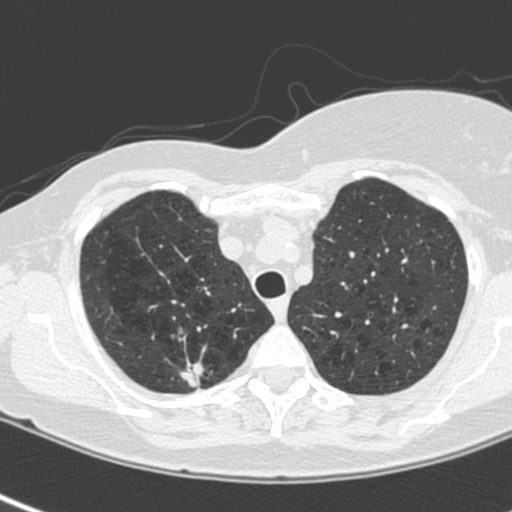
Chest CT (low-dose screening protocol), one axial image. Baseline screening round. Lung window (W 1500 / L -600 HU). 120 kVp. 512 × 512 image matrix. Female participant, aged 64 years at enrolment. Current smoker at enrolment.
Expert reader's lesion annotation, box from (x=167, y=352) to (x=222, y=402) px. The exam's reader record, not a measurement of the box and not confirmed to be the same lesion: non-calcified nodule or mass ≥4 mm, right upper lobe, 13 × 10 mm, spiculated (stellate) margins, soft tissue attenuation. Later outcome: lung cancer diagnosed 21 days after this screen — adenocarcinoma, NOS, right upper lobe, poorly differentiated (G3), stage IIIB (AJCC 6th edition), 20 mm at pathology.